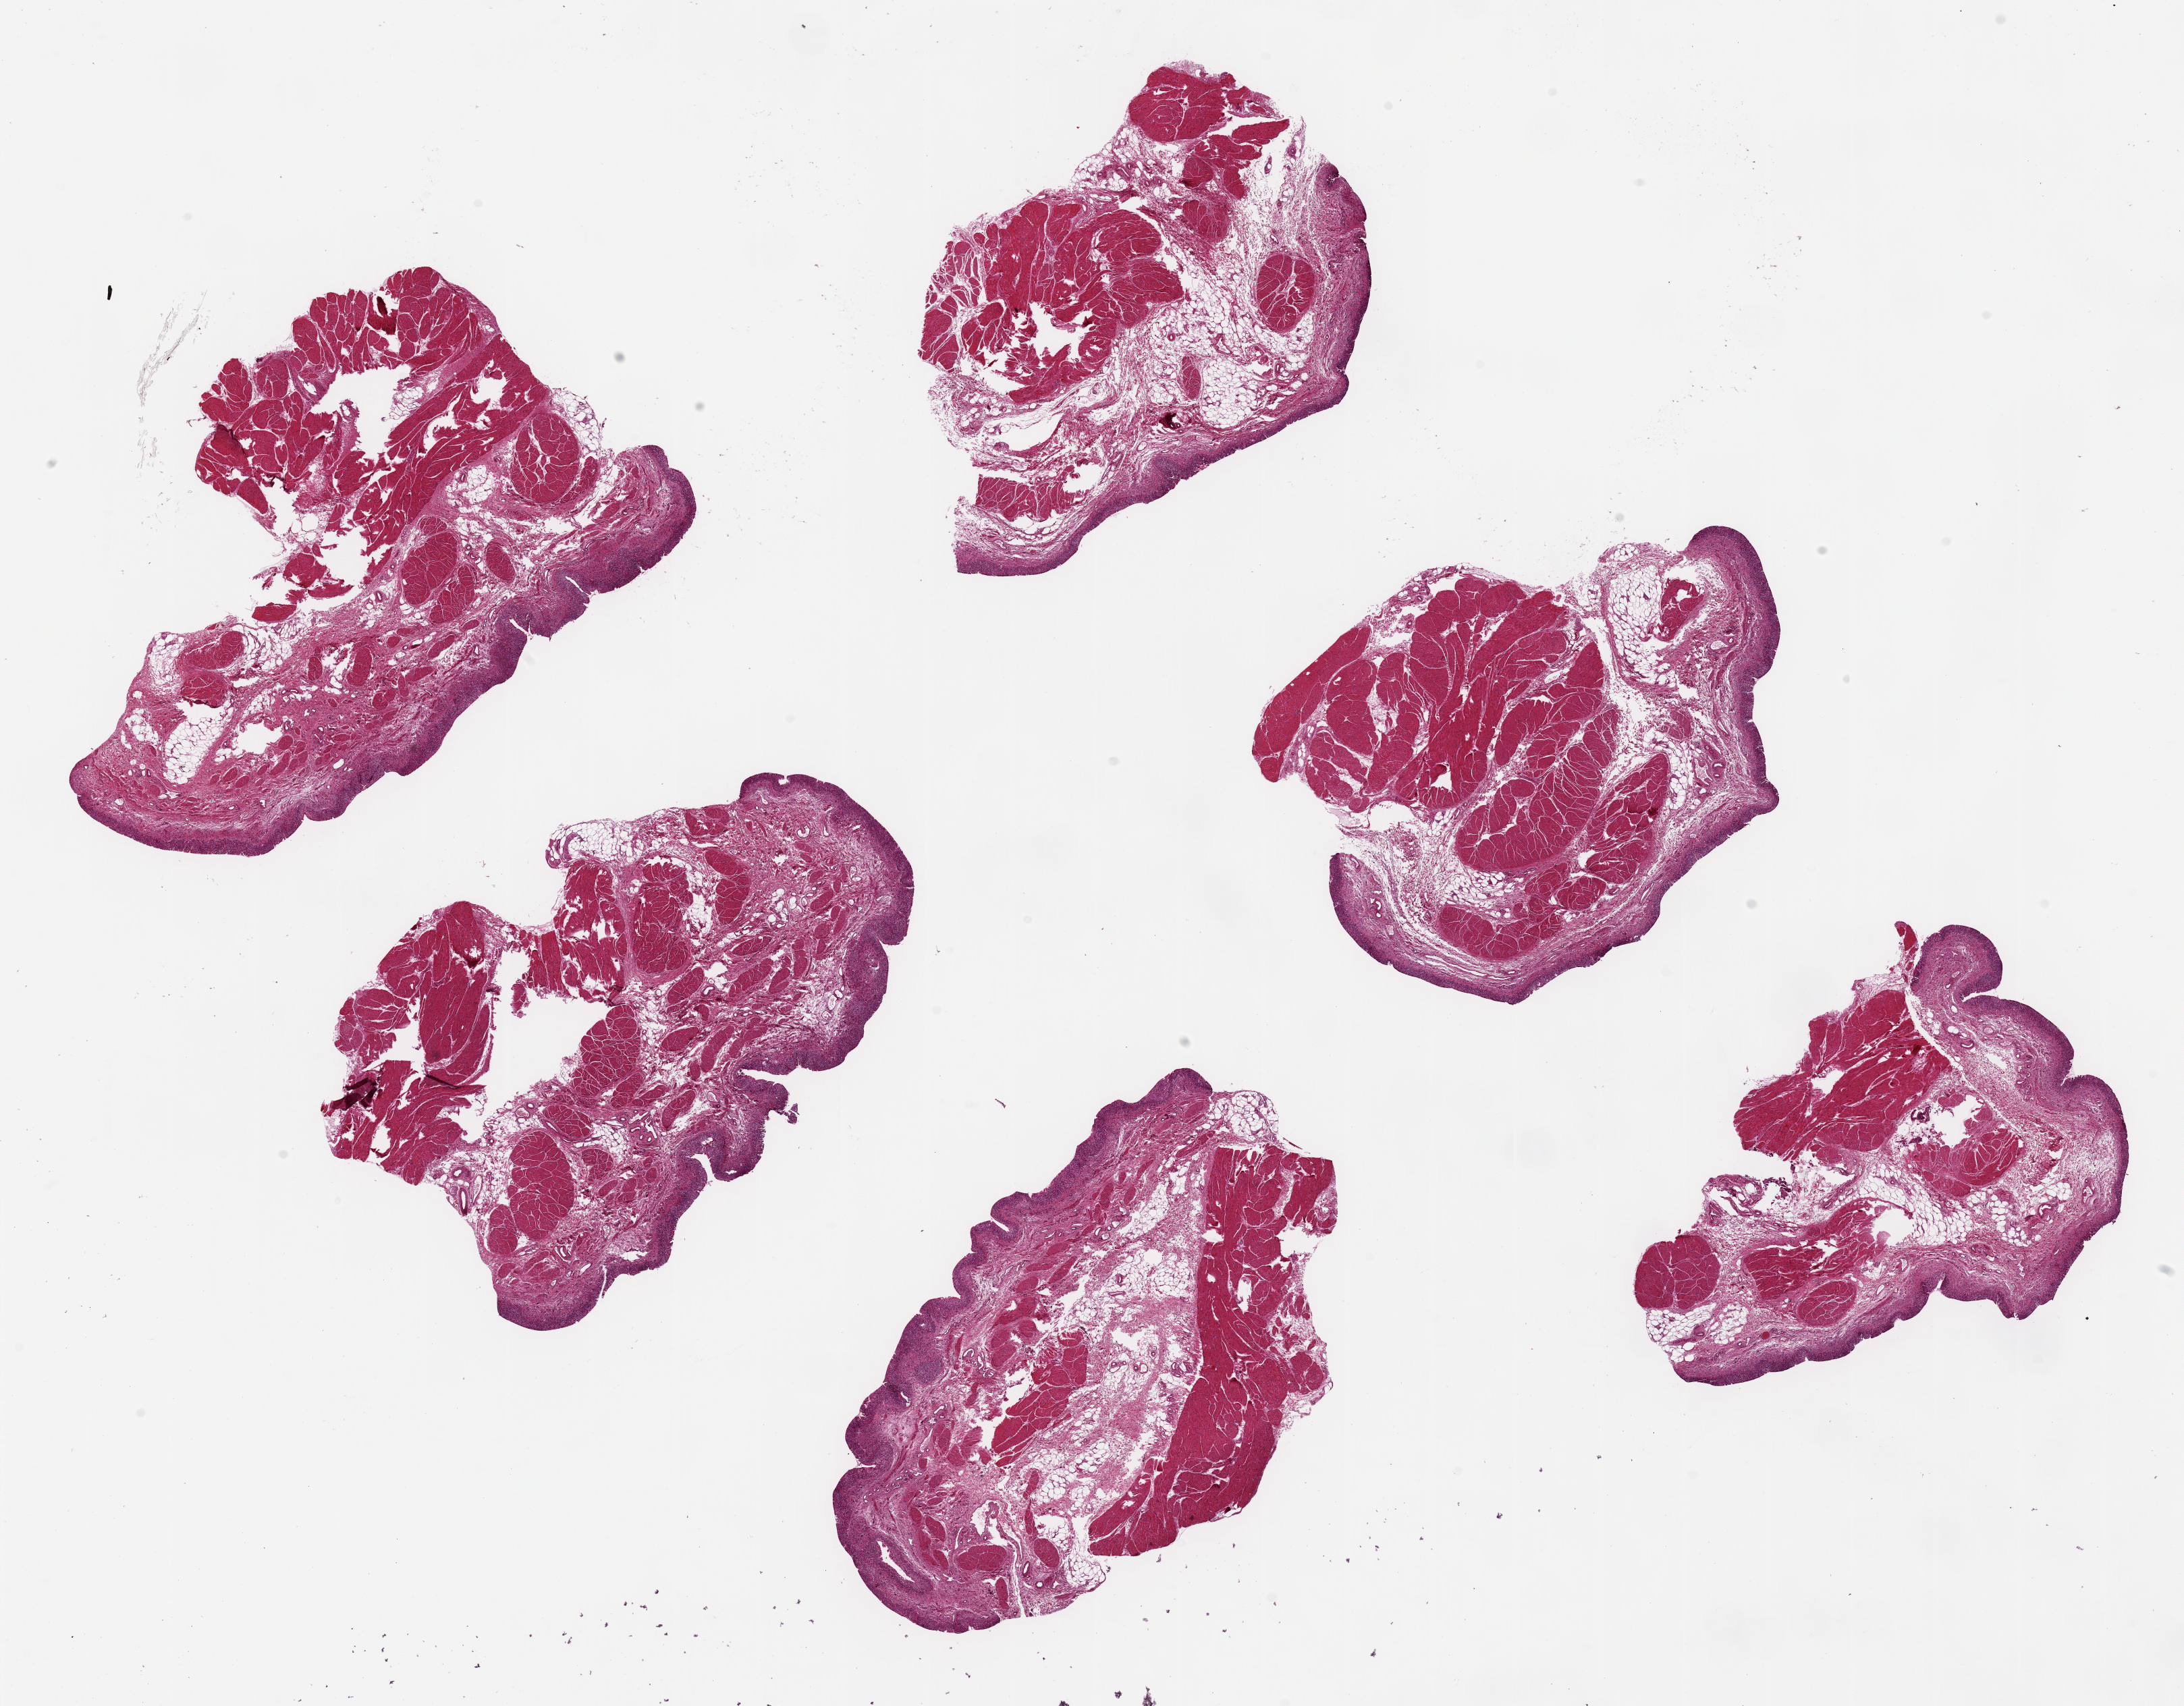
Digitized H&E-stained section, brightfield — a low-resolution overview of the entire scanned area, about 25.6 x 20.0 mm (acquisition: 20x scan). PAXgene-fixed, paraffin-embedded tissue. Section of urinary bladder (target tissue). Tissue donor sample. Male donor.
Reviewer comment on this tissue sample: 6 pieces up to 7x5 mm; epithelial hyperplasia.